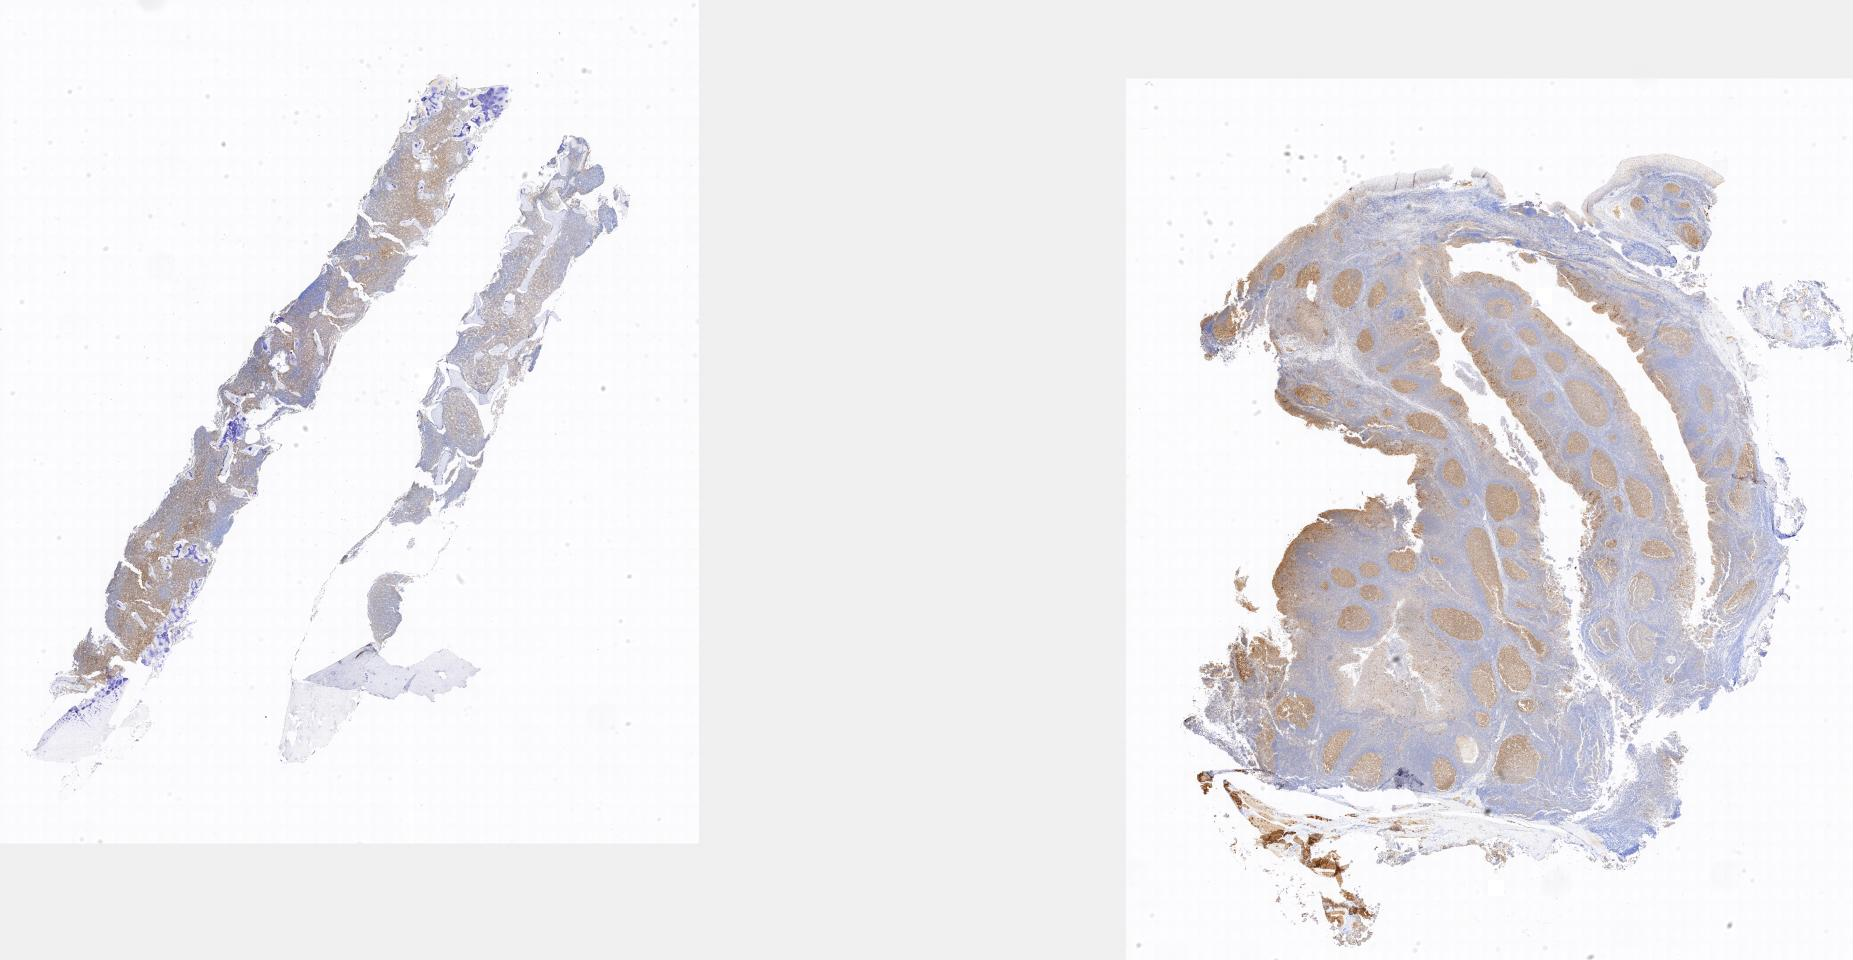
Whole-slide image, immunohistochemical stain for BCL6 — low-resolution overview of the scanned area; specimen: tumor tissue; anatomic site: bone marrow. Patient: male, 16 years old.
* histologic diagnosis: Burkitt lymphoma, NOS